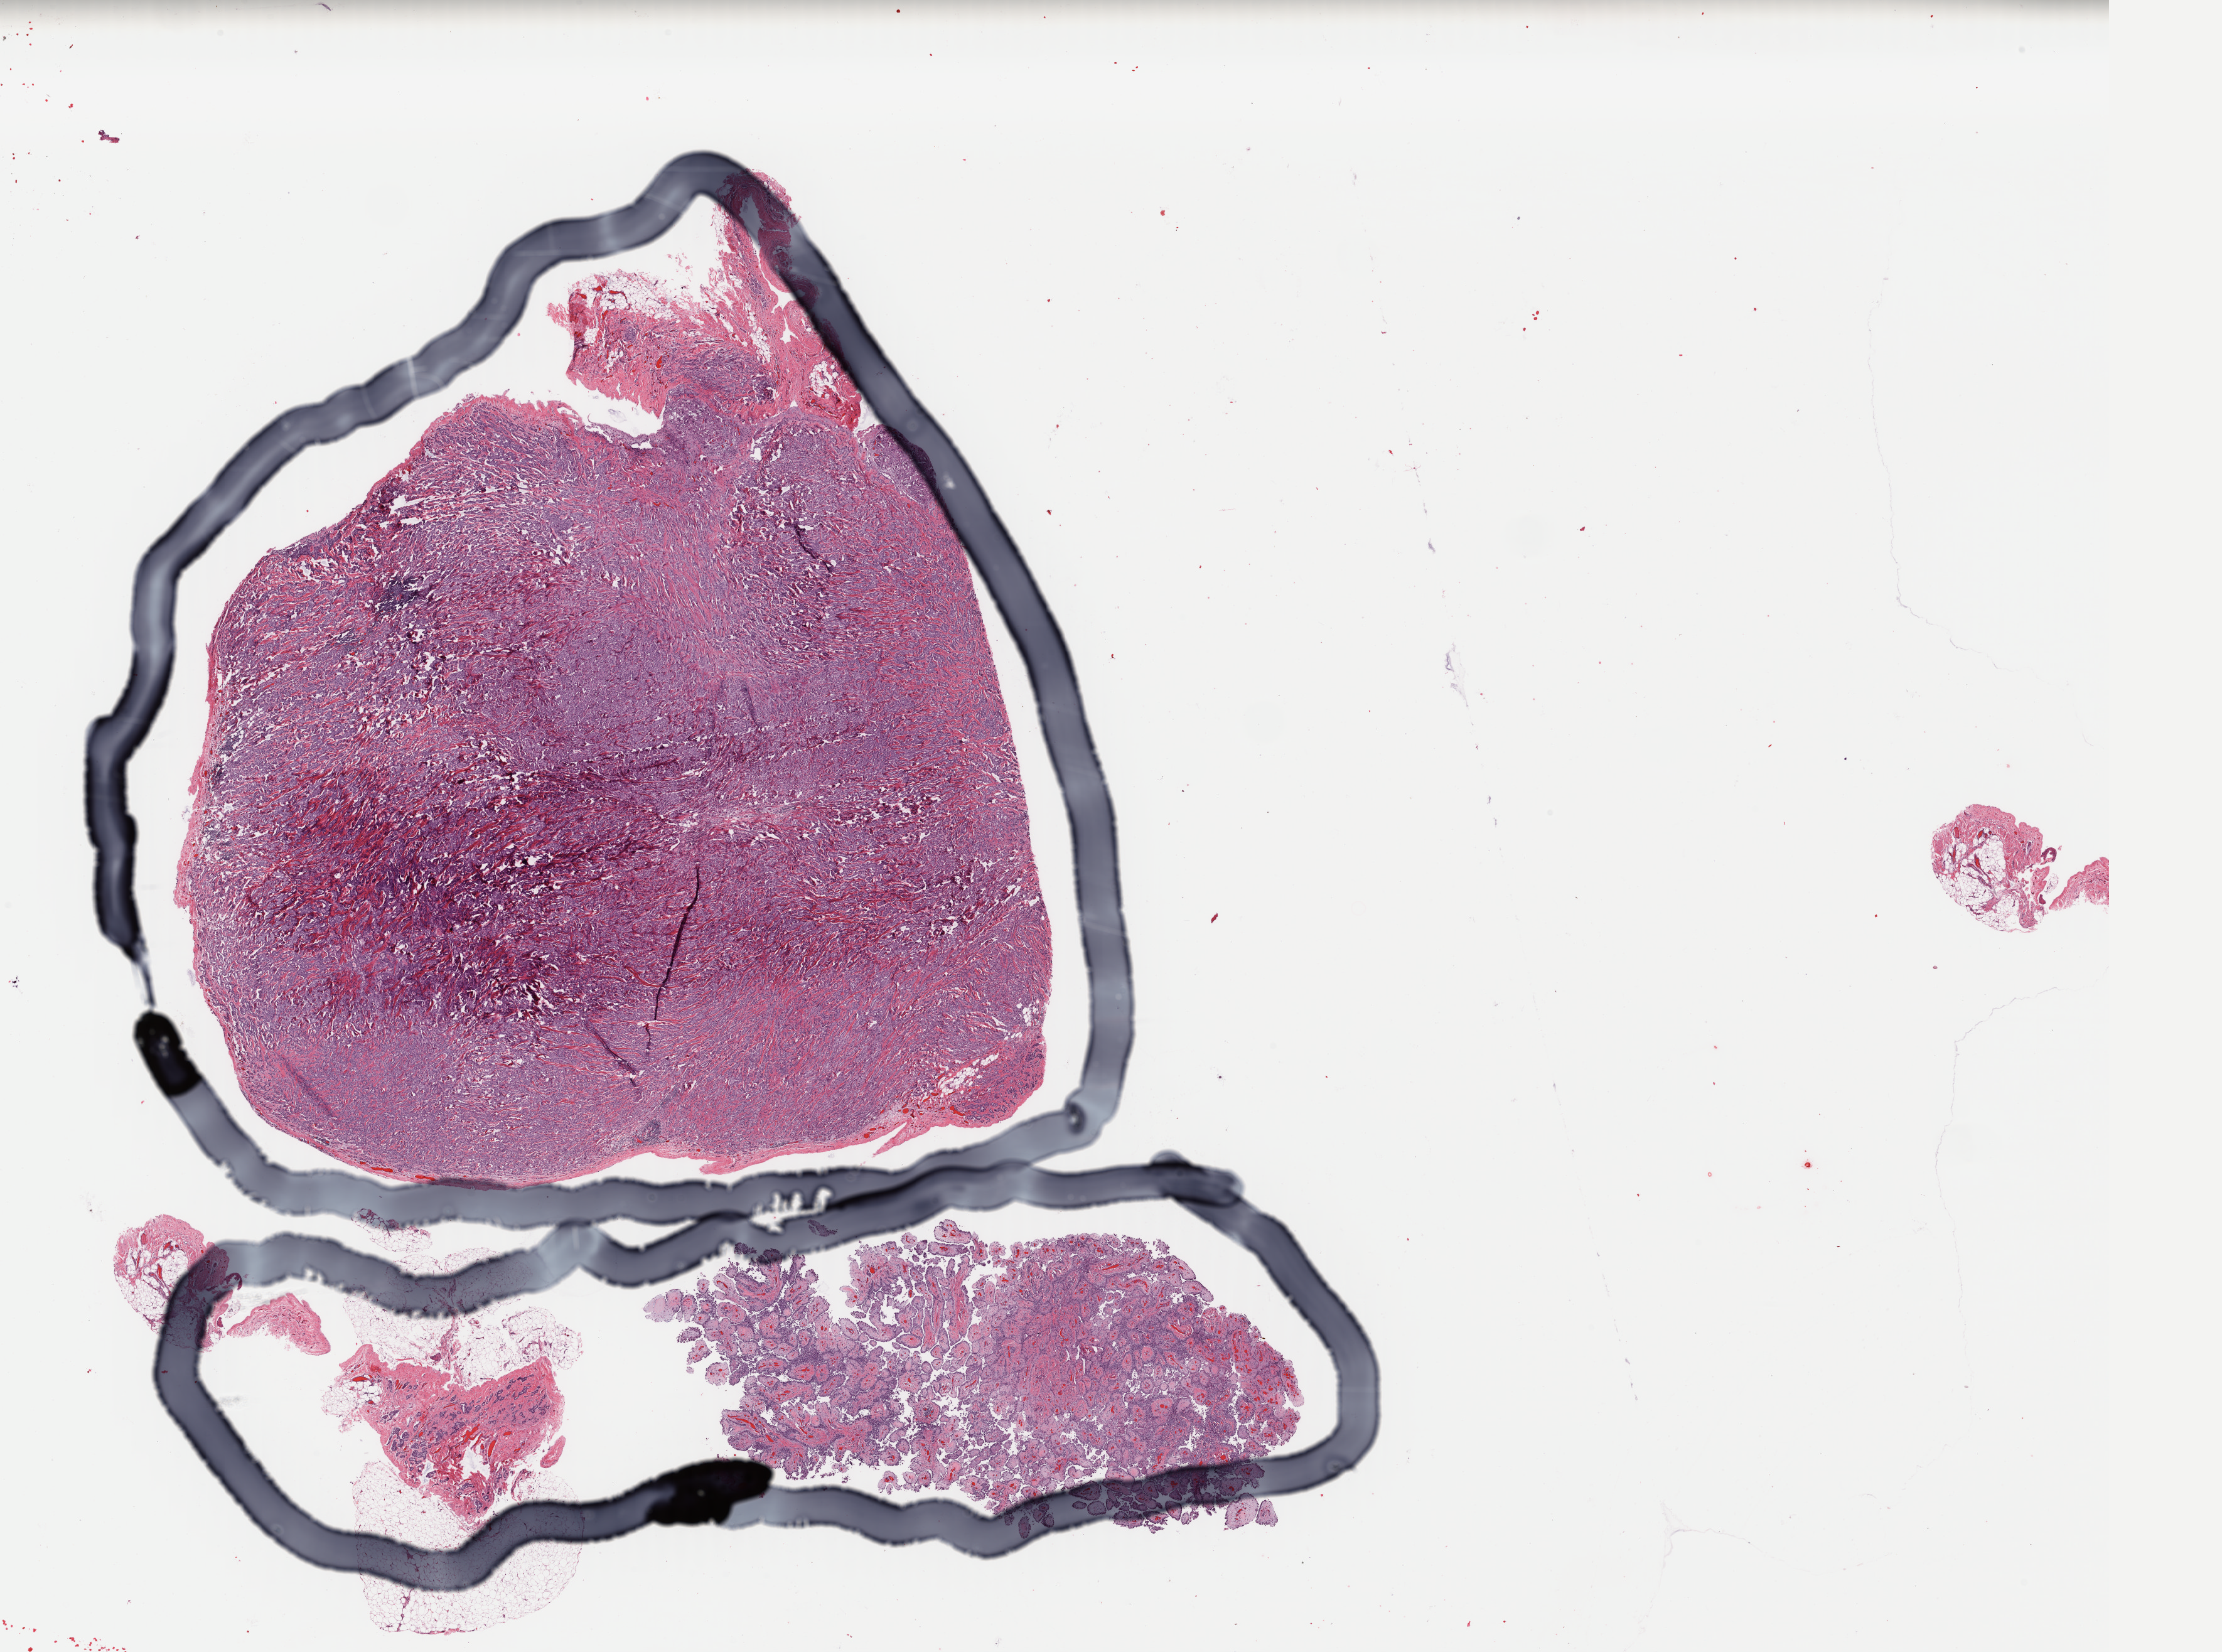
Hematoxylin and eosin (H&E) stained whole-slide image, whole scanned area (about 27.9 x 20.8 mm, acquisition: 40x scan) shown as a low-resolution overview; formalin-fixed paraffin-embedded (FFPE) diagnostic section; sample: primary tumour, mesothelium. Patient: male, age at initial diagnosis 55 years.
AJCC pathologic stage: II (7th edition). Histologic diagnosis: Epithelioid mesothelioma, malignant.